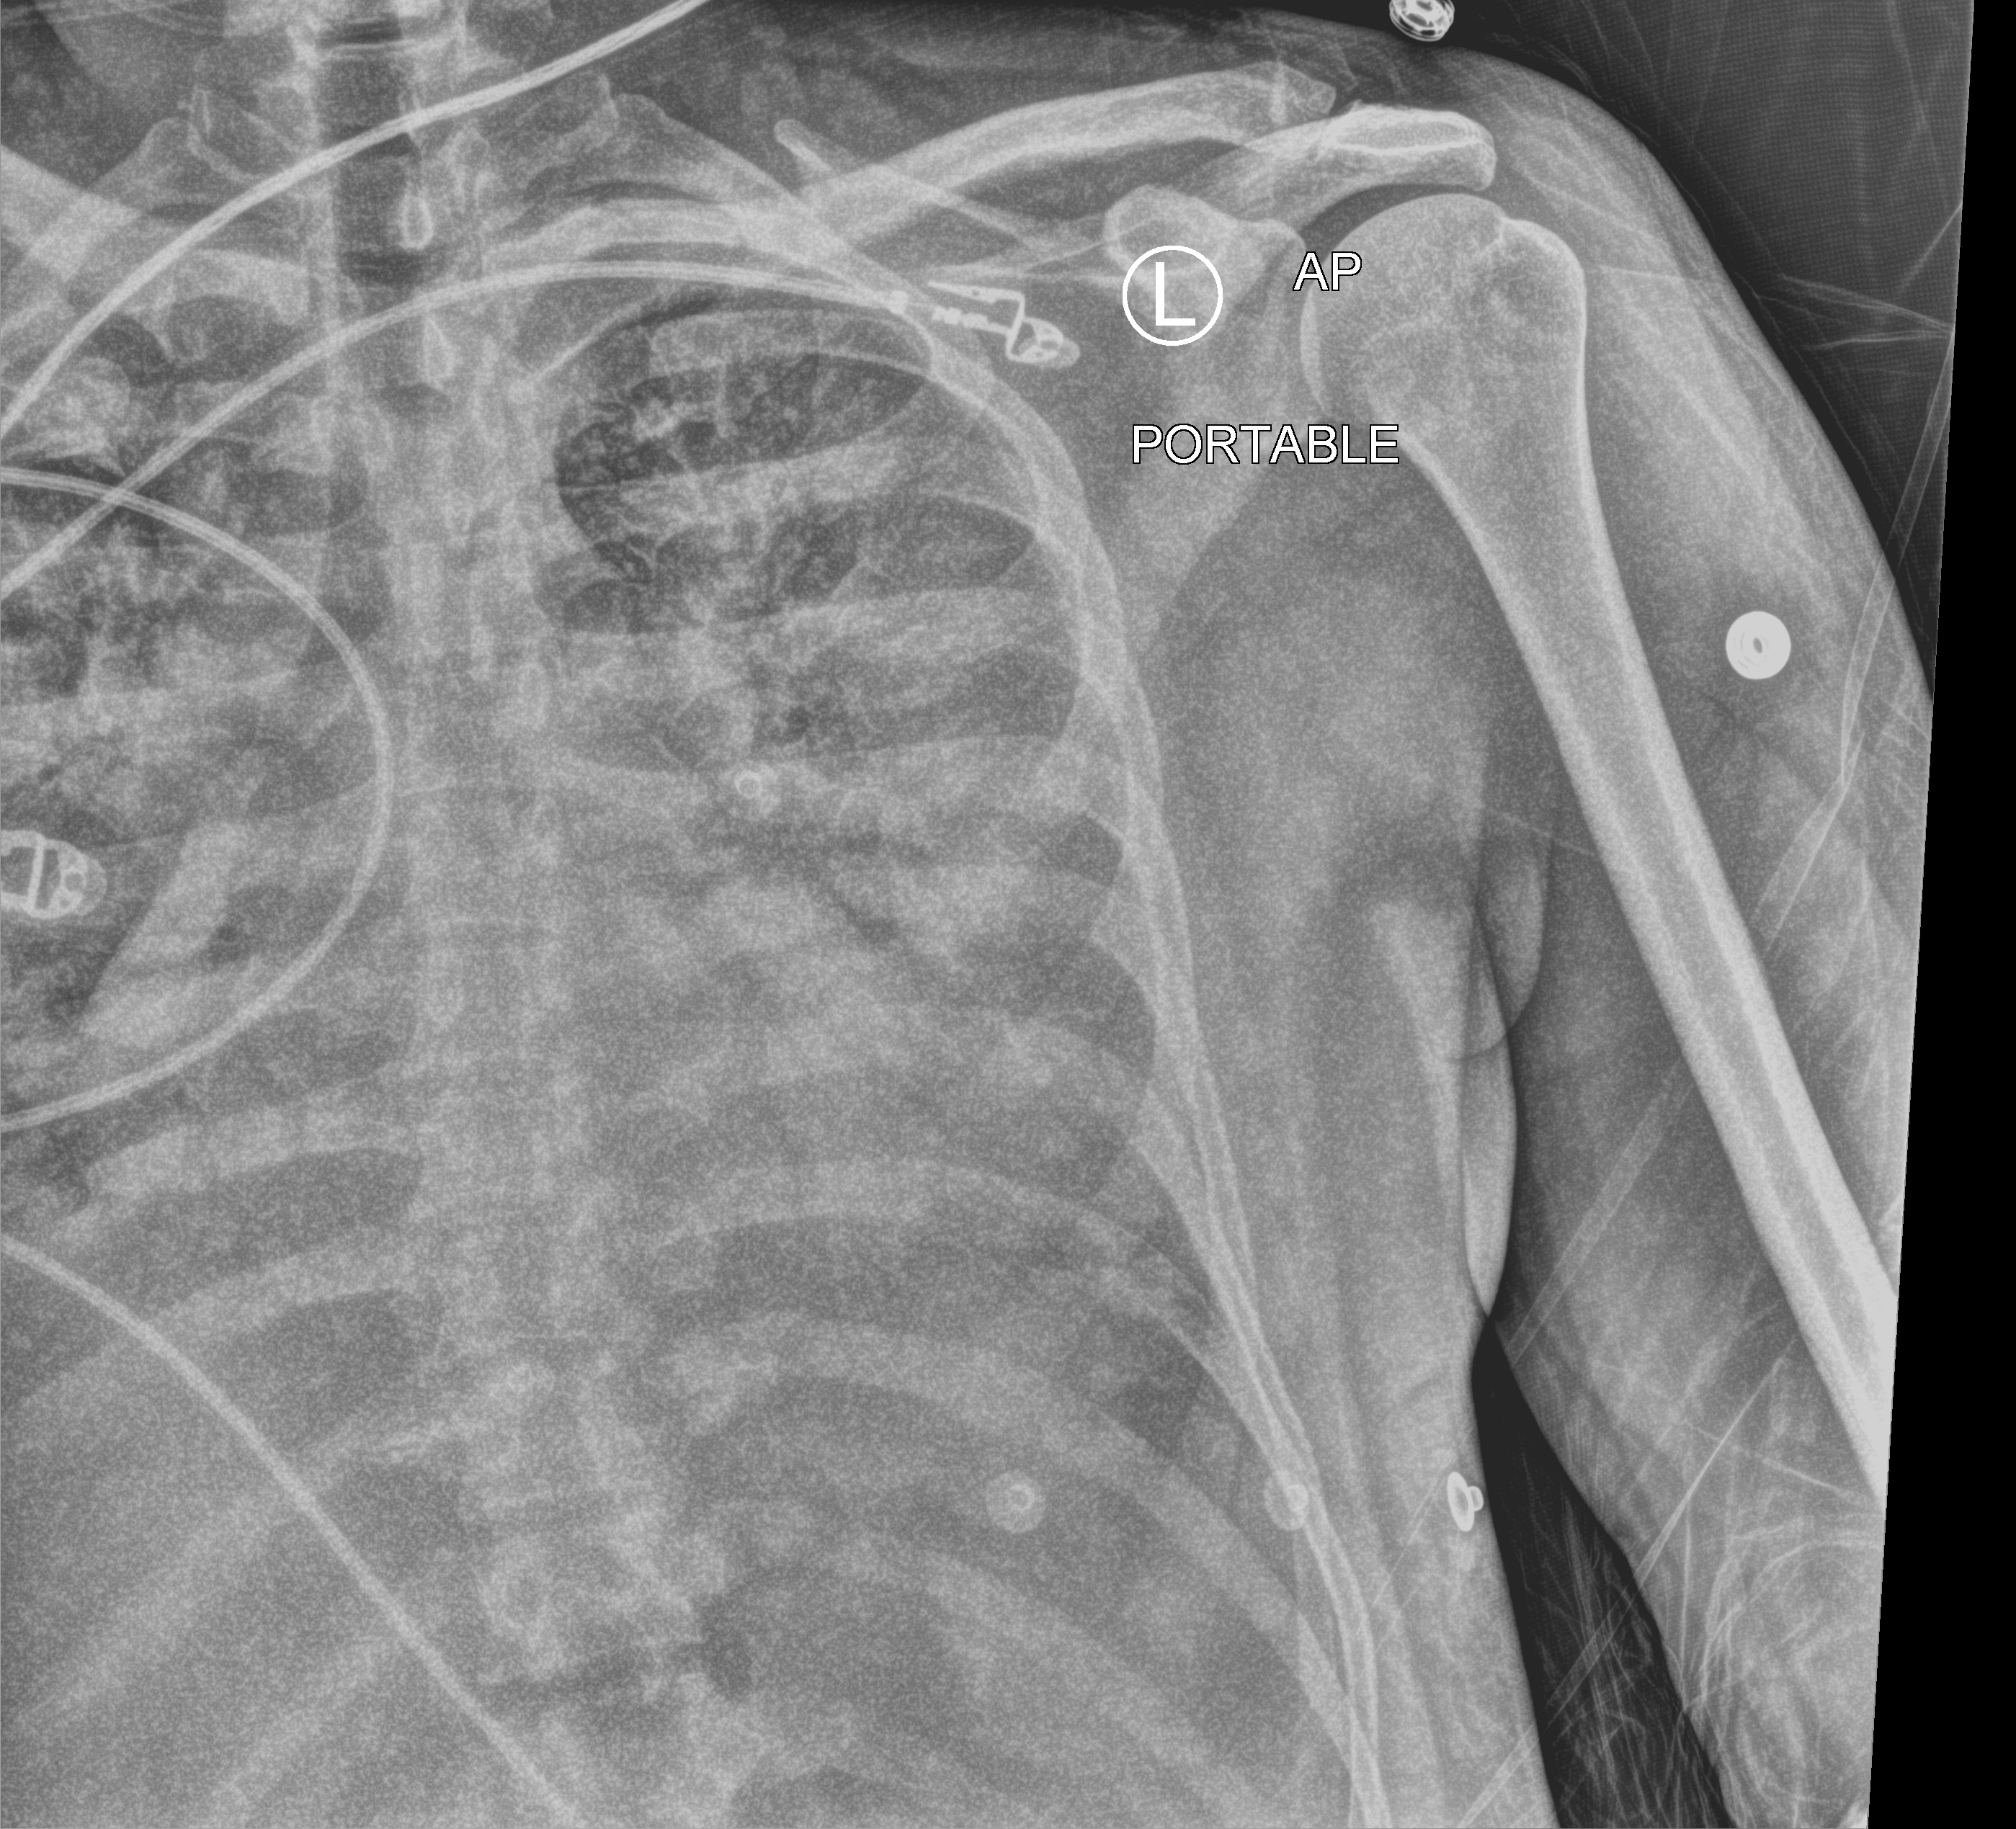
Portable chest radiograph; anteroposterior (AP) projection. Patient hospitalised with COVID-19; male, aged 18–59 years.
From the hospital-stay record, not from the radiograph (when in the stay this image was taken is not recorded): diabetes (admission record): no; admitted to intensive care during this hospital stay: yes; other chronic lung disease (admission record): no.